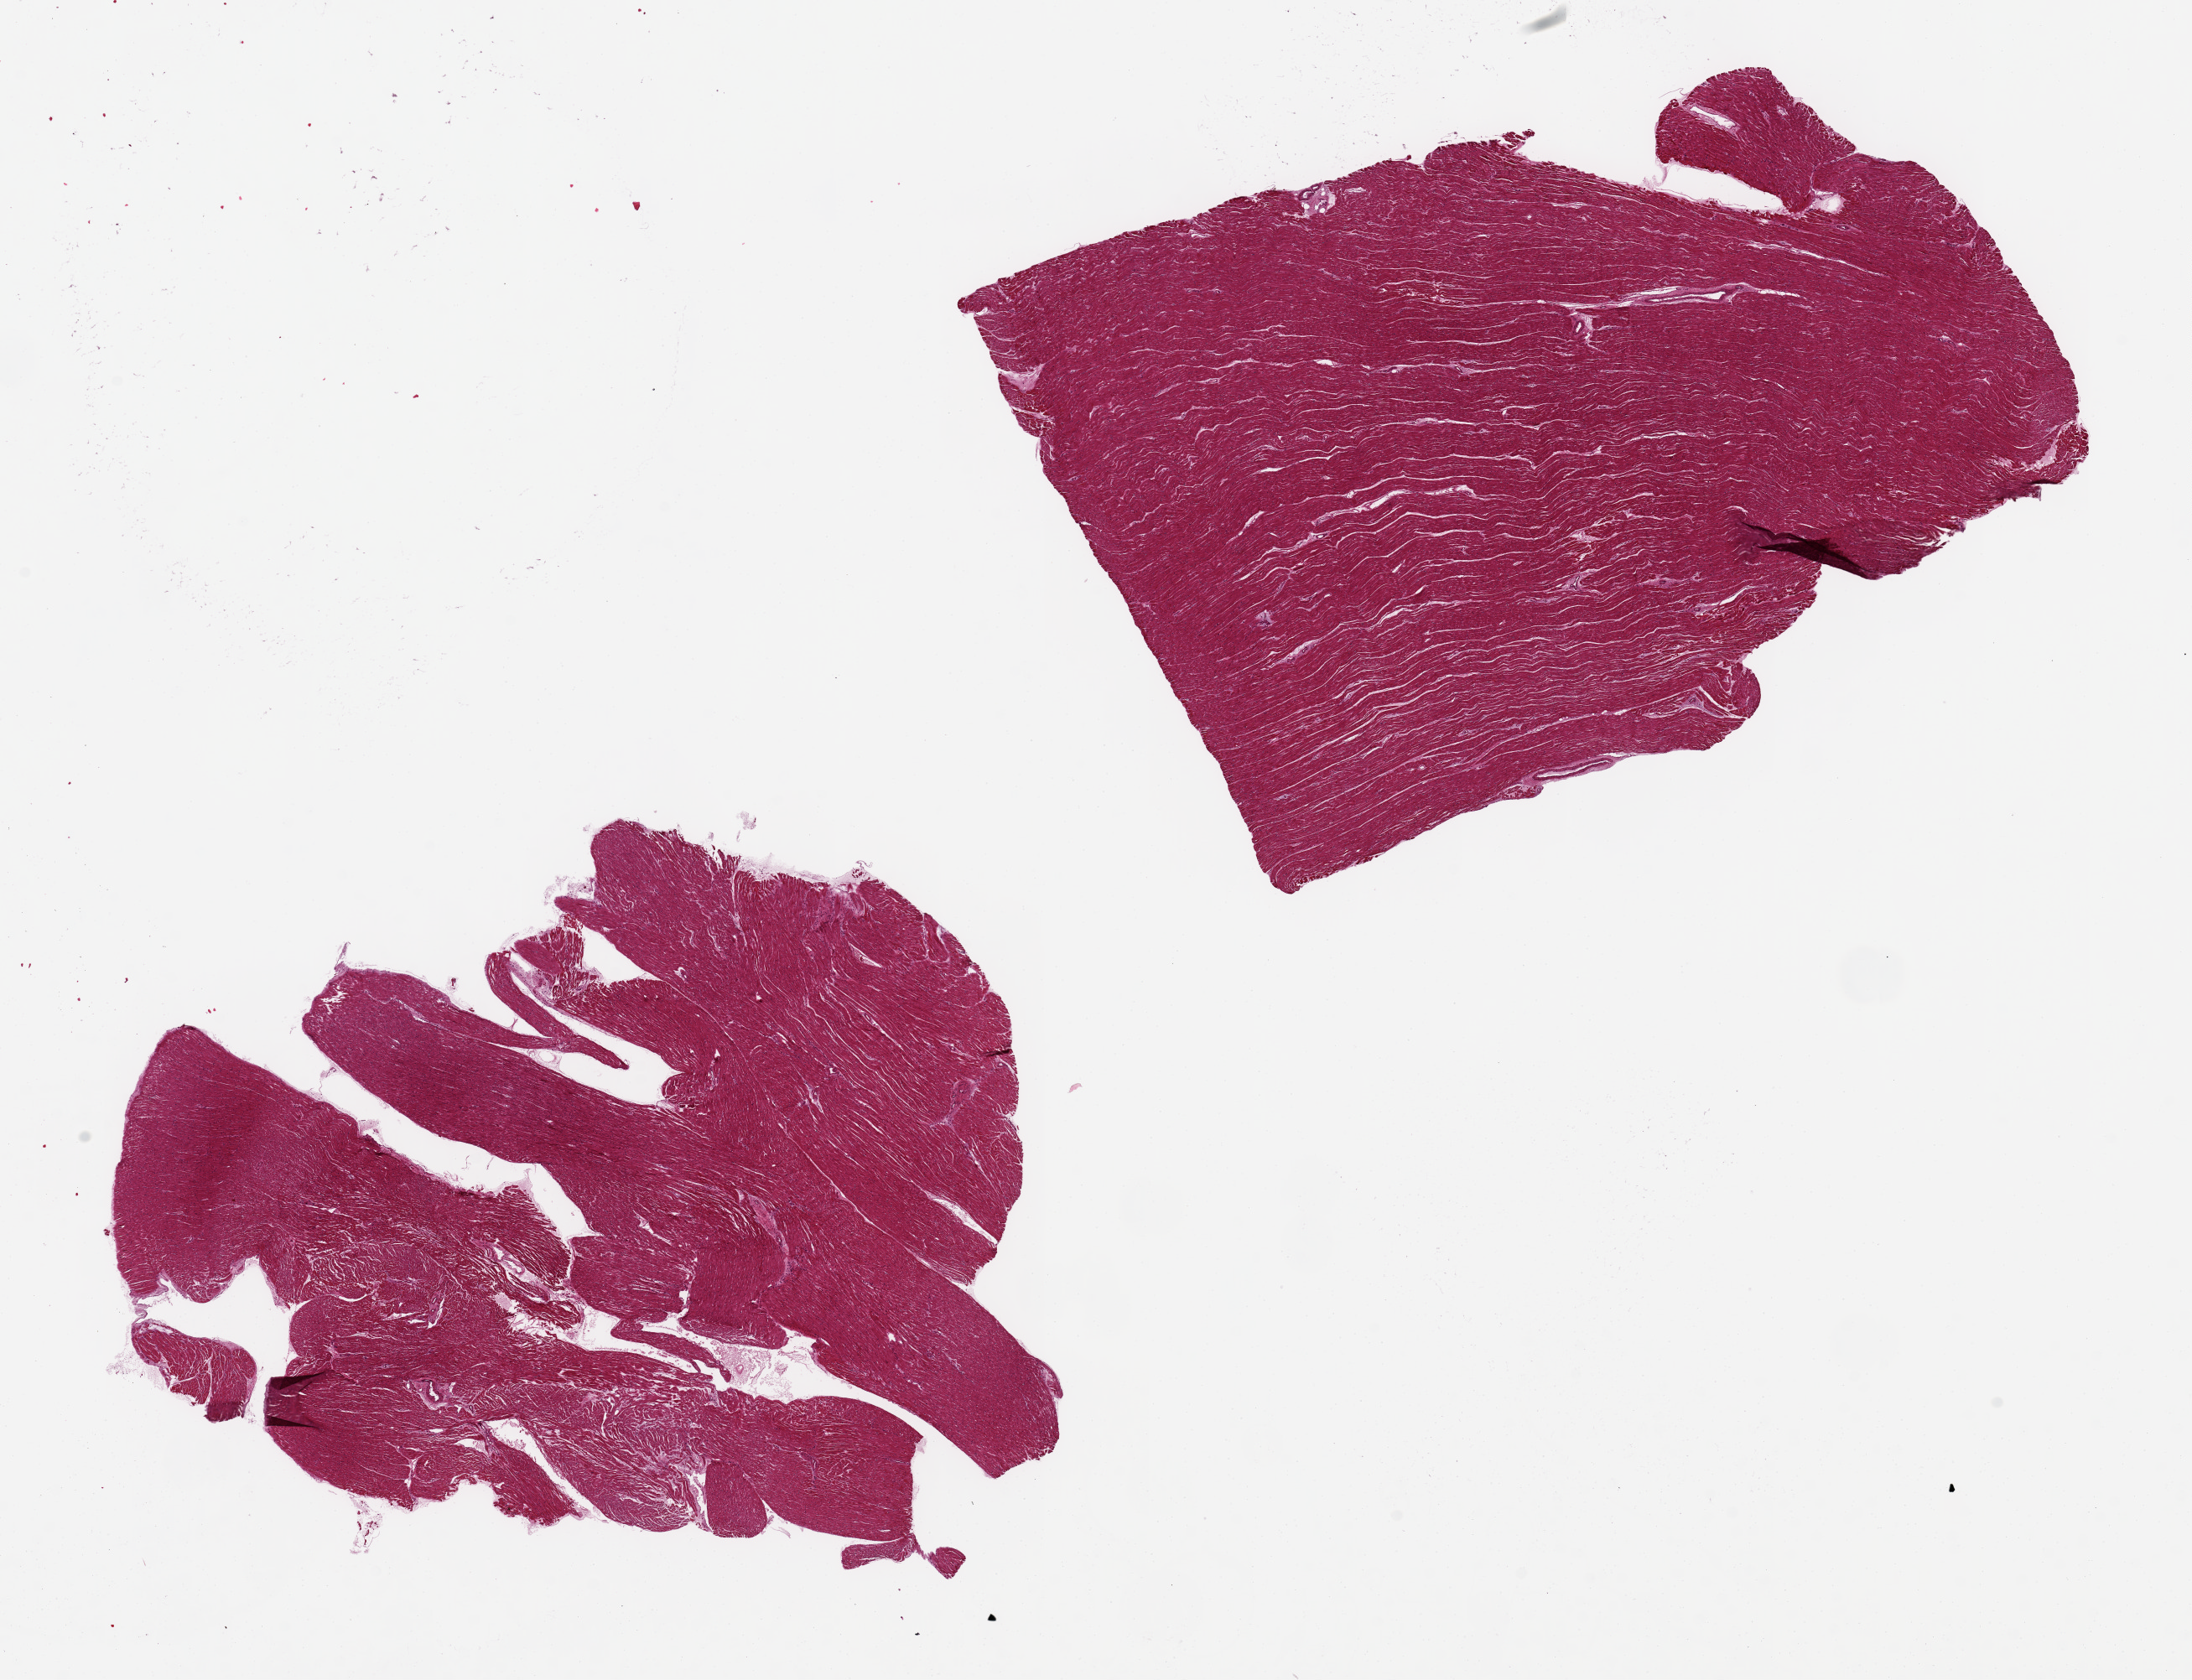
Hematoxylin and eosin (H&E) whole-slide image, whole scanned area (about 20.7 x 15.8 mm, slide scanned at 20x) shown as a low-resolution overview, PAXgene-fixed, paraffin-embedded tissue, section of heart (target tissue), donor tissue sample. Donor sex: male.
Review note (as recorded): 2 pieces ~9x6mm. No ischemic changes.